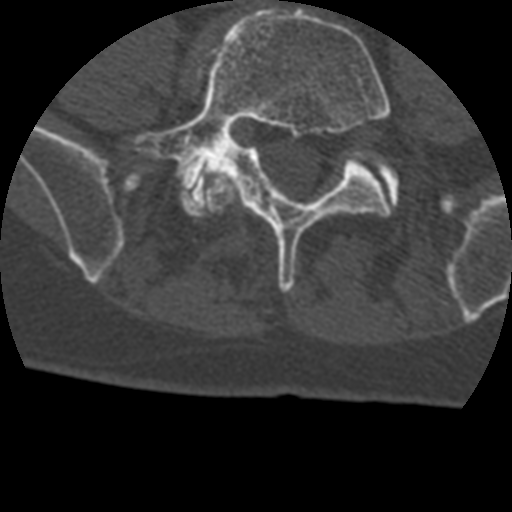
CT including the spine, one axial slice; slice 43 of 399 in the series (ordered by position); reconstruction kernel STANDARD; 120 kVp; bone window (W 1800 / L 400 HU); 1.25 mm slice thickness; 512 × 512 image matrix. Patient age 69 years. From the clinical record (not read from this slice): primary cancer: prostate.
Outlined on this slice (semi-automatically segmented with operator editing):
- L4 vertebra: box from (x=206, y=177) to (x=240, y=214) px
- L5 vertebra: (x=134, y=7)–(x=392, y=292)